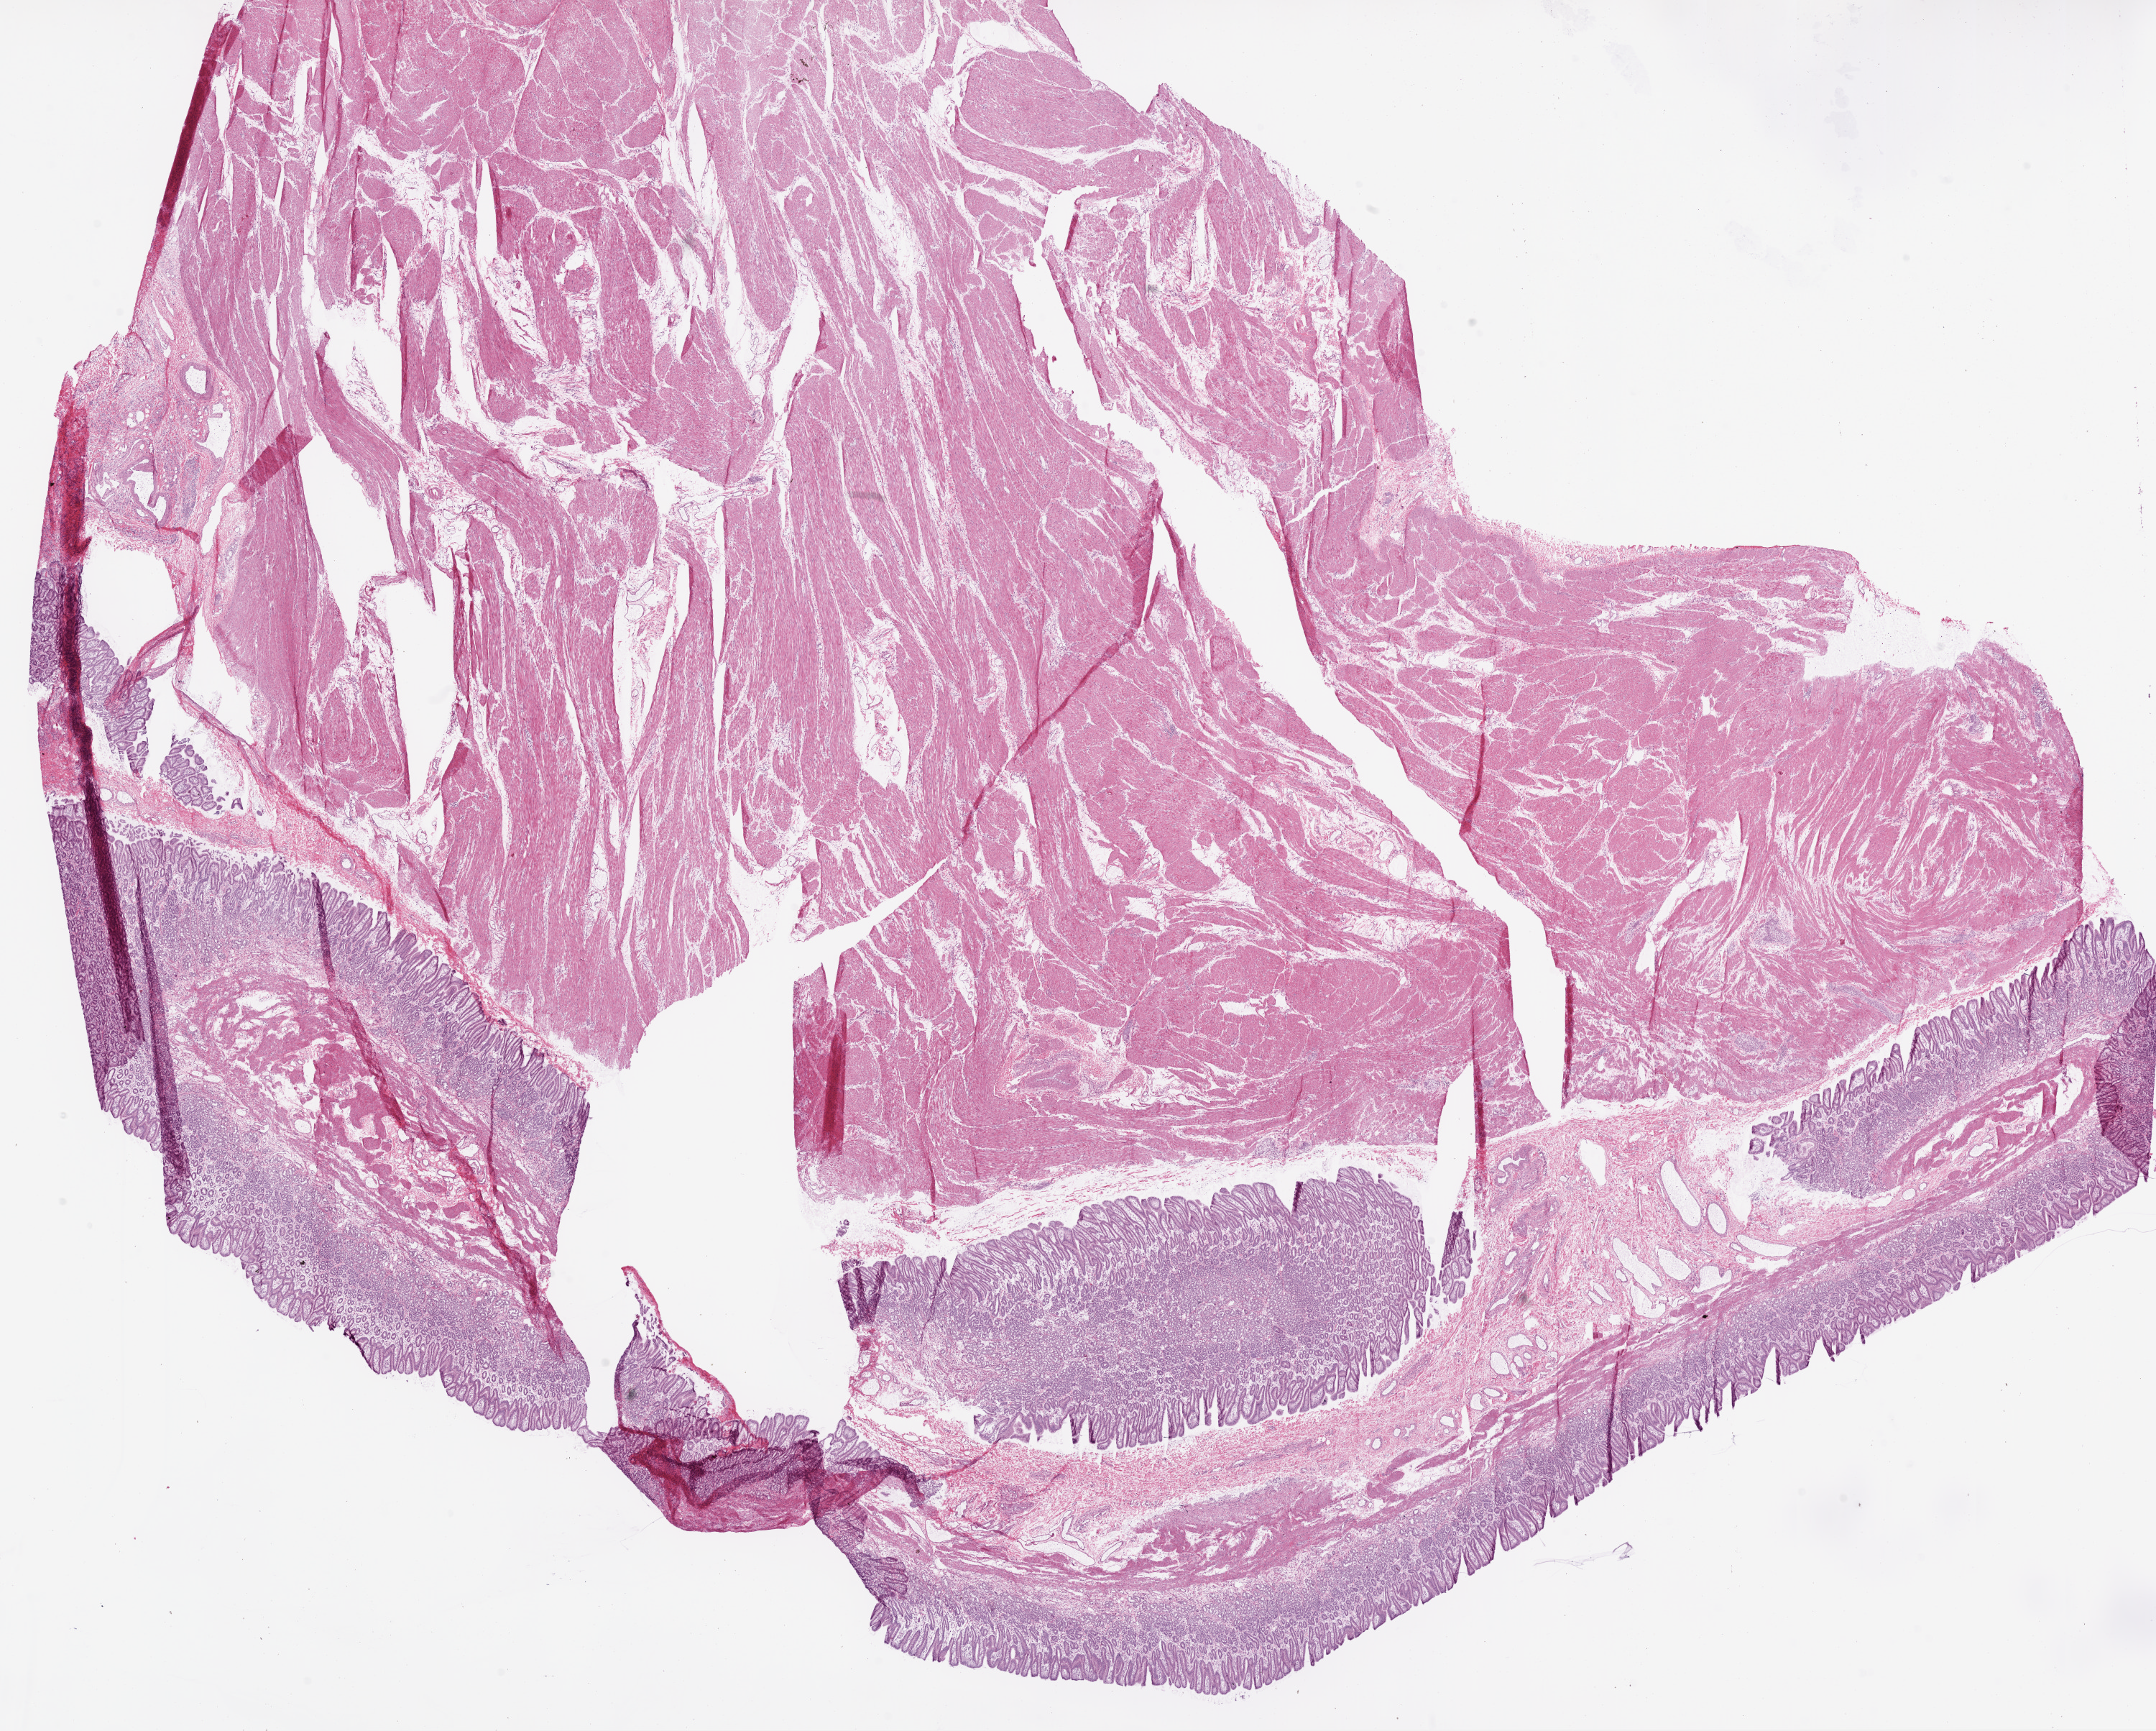
H&E whole-slide image, low-resolution overview of the scanned area, about 24.1 x 19.3 mm. Frozen section from the bottom of the tissue portion. Solid tissue normal (non-tumour tissue) sample from the stomach. Patient: female, age at initial diagnosis 53 years.
This section: solid tissue normal sample (biorepository sample class). Patient diagnosis: Adenocarcinoma, NOS (cardia, NOS).